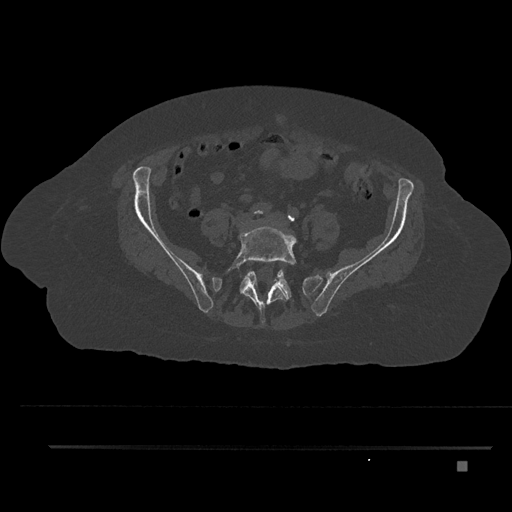
CT including the spine, one axial slice; slice 35 of 797 in the series (ordered by position); 120 kVp; bone window (W 1800 / L 400 HU); 512 × 512 image matrix, field of view 437 × 437 mm. Patient: female, 76 years. From the clinical record (not read from this slice): primary cancer: lung.
Outlined on this slice (semi-automatically segmented with operator editing):
- L5 vertebra: bounding box [x1, y1, x2, y2] px = [232, 226, 297, 324]